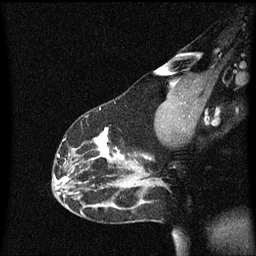
Breast MRI (dynamic contrast-enhanced), one sagittal slice; position 39 of 60 along the scan axis; dynamic contrast-enhanced series, image 2 of 3 at this slice position (ordered by acquisition); 1.5 T; TE 4.2 ms, TR 8.4 ms; 2 mm slice thickness; 256 × 256 image matrix. Female patient, age 33 years.
Outlined on this slice (semi-automatic segmentation, software-assisted and operator-edited):
- analysis volume of interest (the breast-tissue region the enhancement analysis was run in; not a lesion): bounding box [x1, y1, x2, y2] px = [53, 114, 152, 191]
- tumour enhancement mask (voxels above the 70 % enhancement threshold inside the analysis volume of interest): [55, 128, 148, 181]